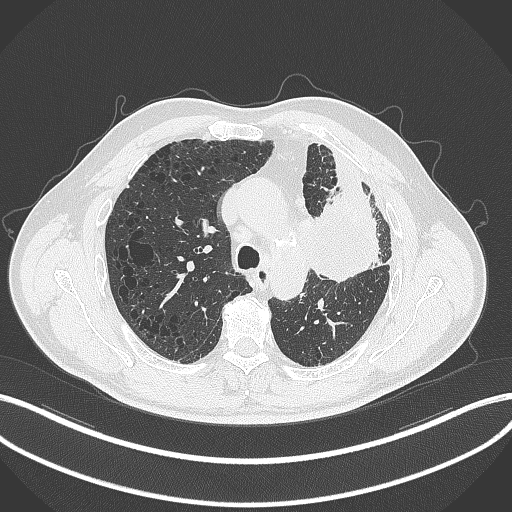
Chest CT, one axial slice. Position 217 of 297 along the scan axis. Reconstruction kernel B70f. 120 kVp. Lung window (W 1500 / L -600 HU). 1 mm slice thickness. 512 × 512 image matrix, field of view 400 × 400 mm. Patient: male, 68 years. Case-level facts recorded for this patient, not image findings: clinical TNM (as recorded): T3 N3 M1.
Outlined on this slice (rectangle marked by the reading radiologist):
- lung tumour (recorded histology: adenocarcinoma): bounding box (x1, y1, x2, y2) in pixels: (308, 171, 387, 289)